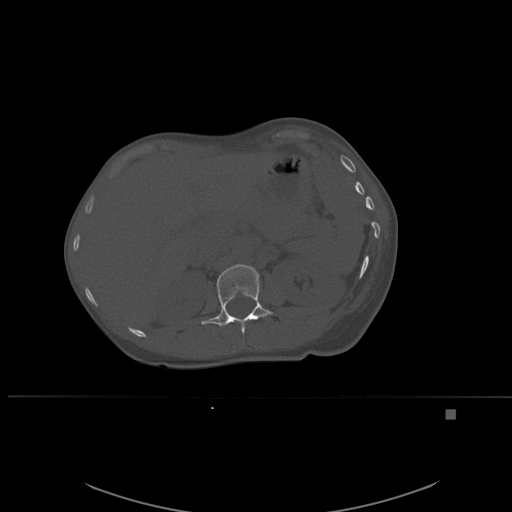
CT including the spine, one axial slice. Slice 261 of 537 in the series (ordered by position). Bone window (W 1800 / L 400 HU). 1.5 mm slice thickness. 512 × 512 image matrix, field of view 440 × 440 mm. Female patient, age 45 years. Case-level facts recorded for this patient, not image findings: primary cancer: lung.
Structures marked on this image (semi-automatic segmentation, software-assisted and operator-edited):
- L1 vertebra: bounding box [x1, y1, x2, y2] px = [201, 264, 274, 335]